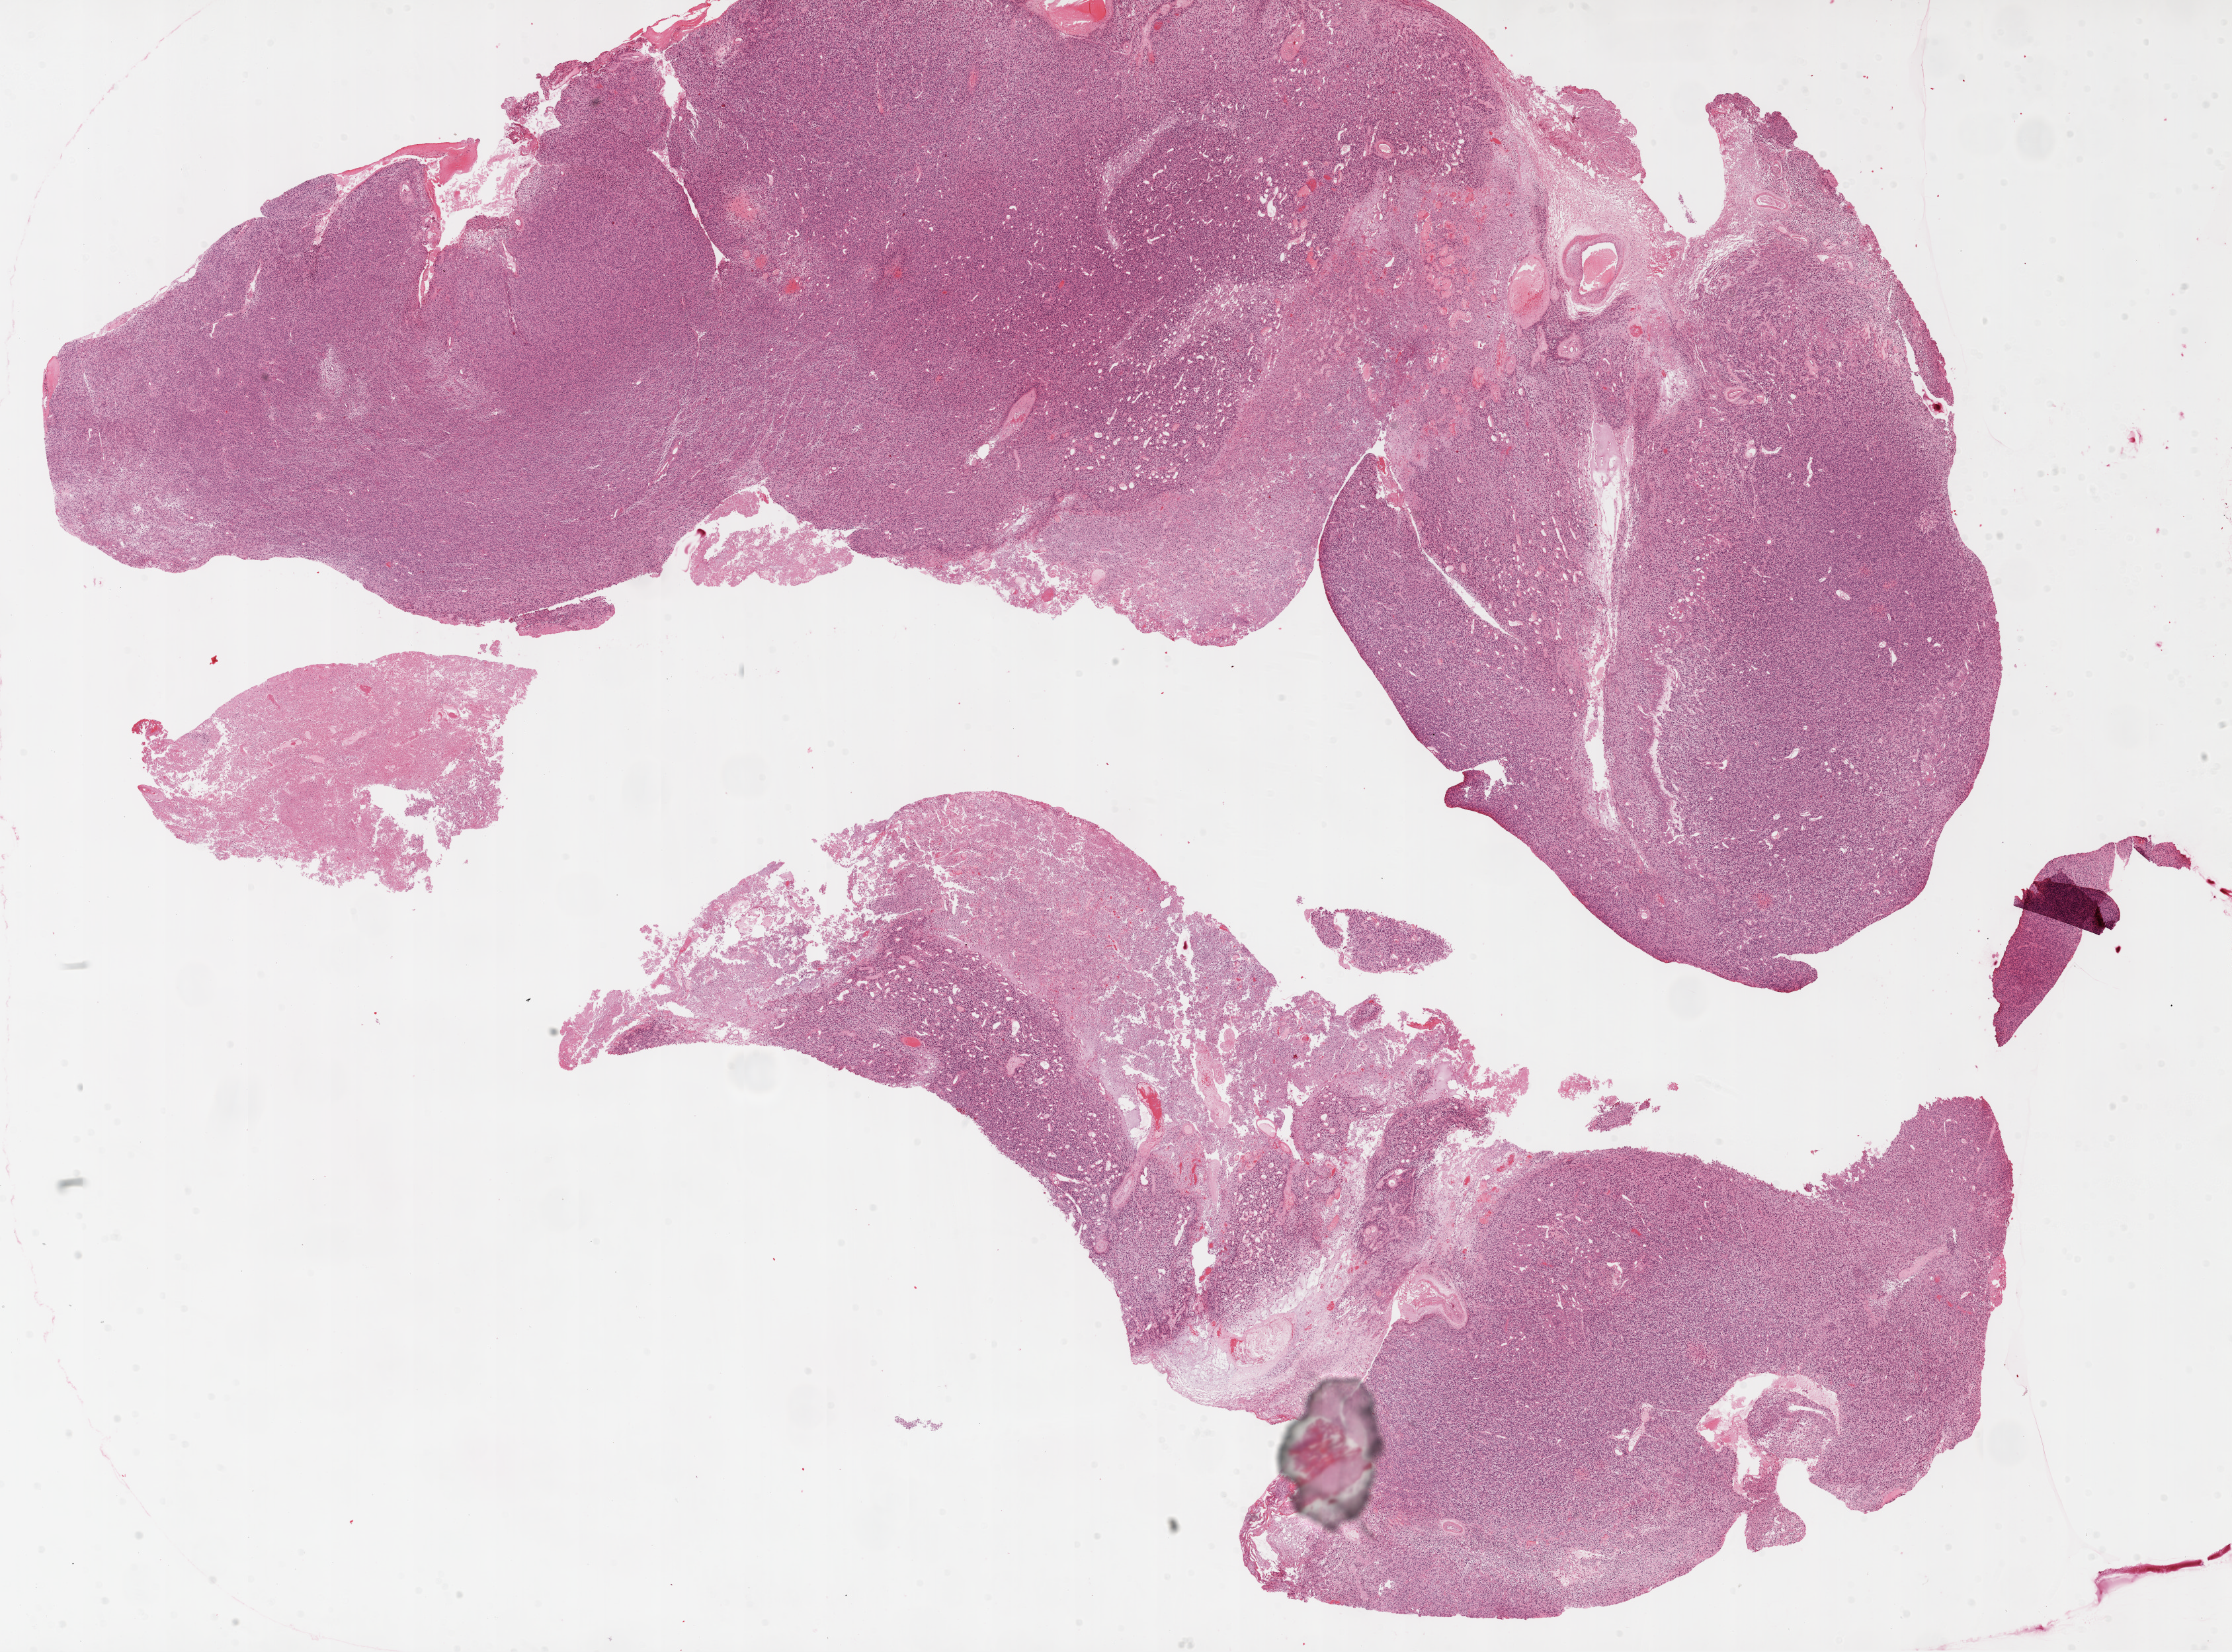
Whole-slide histology image, Hematoxylin and eosin (H&E) stained — shown as a low-resolution overview of the whole scanned area (about 27.1 x 20.0 mm, slide scanned at 20x). Formalin-fixed paraffin-embedded (FFPE) diagnostic section. Brain, primary tumour sample. Patient: female, age at initial diagnosis 67 years.
Pathologic diagnosis: Glioblastoma.